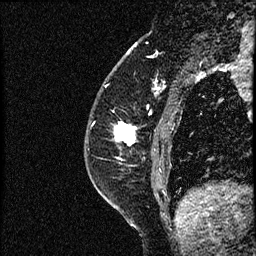
Breast MRI (dynamic contrast-enhanced), one sagittal slice; position 19 of 52 along the scan axis; dynamic contrast-enhanced study with each time point stored as its own series, time point 2 of 3 at this slice position (early post-contrast, ordered by acquisition time); 1.5 T; TE 4.2 ms, TR 17.6 ms; 2 mm slice thickness; 256 × 256 image matrix, field of view 200 × 200 mm. Female patient, age 49 years. From the clinical record (not read from this slice): setting: breast cancer imaged before/during neoadjuvant chemotherapy; receptor status: HER2-positive.
Annotated regions visible in this slice (semi-automatic segmentation, software-assisted and operator-edited):
- analysis volume of interest (the breast-tissue region the enhancement analysis was run in; not a lesion): bounding box <85,65,182,175> (left, top, right, bottom; pixels)
- tumour enhancement mask (voxels above the 100 % enhancement threshold inside the analysis volume of interest): <116,123,136,146>